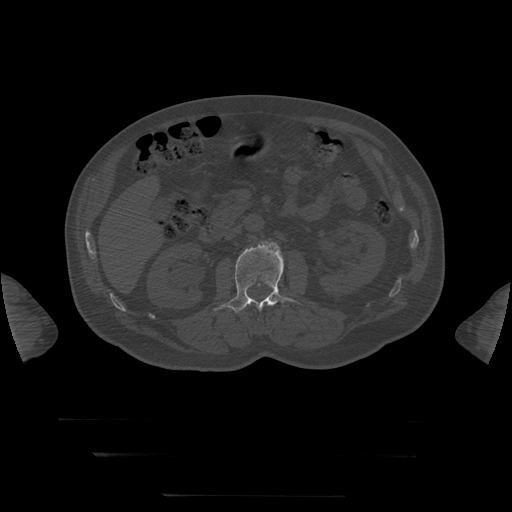
CT including the spine, one axial slice. Slice 24 of 397 in the series (ordered by position). Reconstruction kernel STANDARD. Bone window (W 1800 / L 400 HU). 1.25 mm slice thickness. 512 × 512 image matrix, field of view 510 × 510 mm. Patient age 73 years. From the clinical record (not read from this slice): primary cancer: prostate.
Structures marked on this image (semi-automatically segmented with operator editing):
- L1 vertebra: bounding box (x1, y1, x2, y2) in pixels: (249, 302, 268, 308)